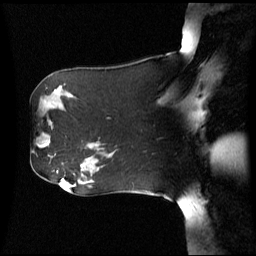
Breast MRI (dynamic contrast-enhanced), one sagittal slice; slice 38 of 60 in the series (ordered by position); dynamic contrast-enhanced series, image 2 of 3 at this slice position (ordered by acquisition); 1.5 T; TE 4.2 ms, TR 8.4 ms; 2.5 mm slice thickness; 256 × 256 image matrix, field of view 260 × 260 mm. Patient: female, 62 years. Case-level facts recorded for this patient, not image findings: setting: breast cancer imaged before/during neoadjuvant chemotherapy; receptor status: HR-positive, HER2-negative.
Outlined on this slice (semi-automatically segmented with operator editing):
- analysis volume of interest (the breast-tissue region the enhancement analysis was run in; not a lesion): box from (x=31, y=119) to (x=57, y=159) px
- tumour enhancement mask (voxels above the 70 % enhancement threshold inside the analysis volume of interest): (x=44, y=144)–(x=50, y=148)